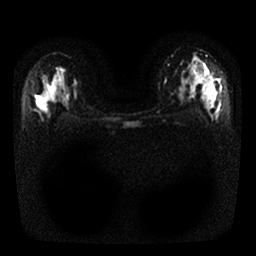
Breast MRI, one axial slice; position 17 of 25 along the scan axis; diffusion-weighted series; image 2 of 4 stored at this slice position (different b-values; order by instance number); 1.5 T; 256 × 256 image matrix, field of view 320 × 320 mm. Female patient.
Structures marked on this image (outlined manually by an expert reader):
- tumour on diffusion-weighted imaging: bounding box <199,72,216,106> (left, top, right, bottom; pixels)